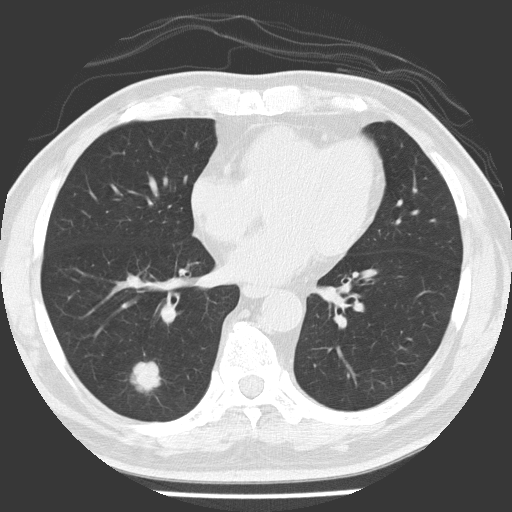
Axial slice from a low-dose chest CT screening exam. First (baseline) screen. Lung window (W 1500 / L -600 HU). 2 mm slice thickness. Lung (sharp) reconstruction kernel (FC51). Slice 88 of 154 in the series. 512 × 512 image matrix, field of view 311 × 311 mm. Male, age 56 years at enrolment. Former smoker at enrolment.
Expert-annotated lung lesion, box from (x=117, y=353) to (x=168, y=404) px. Reader record for this screening exam (exam-level; its link to the box is not recorded): non-calcified nodule or mass ≥4 mm, right lower lobe, 21 × 17 mm, spiculated (stellate) margins, soft tissue attenuation. Later outcome: lung cancer diagnosed 84 days after this screen — adenocarcinoma, NOS, right lower lobe, poorly differentiated (G3), stage IA (AJCC 6th edition), 24 mm at pathology.